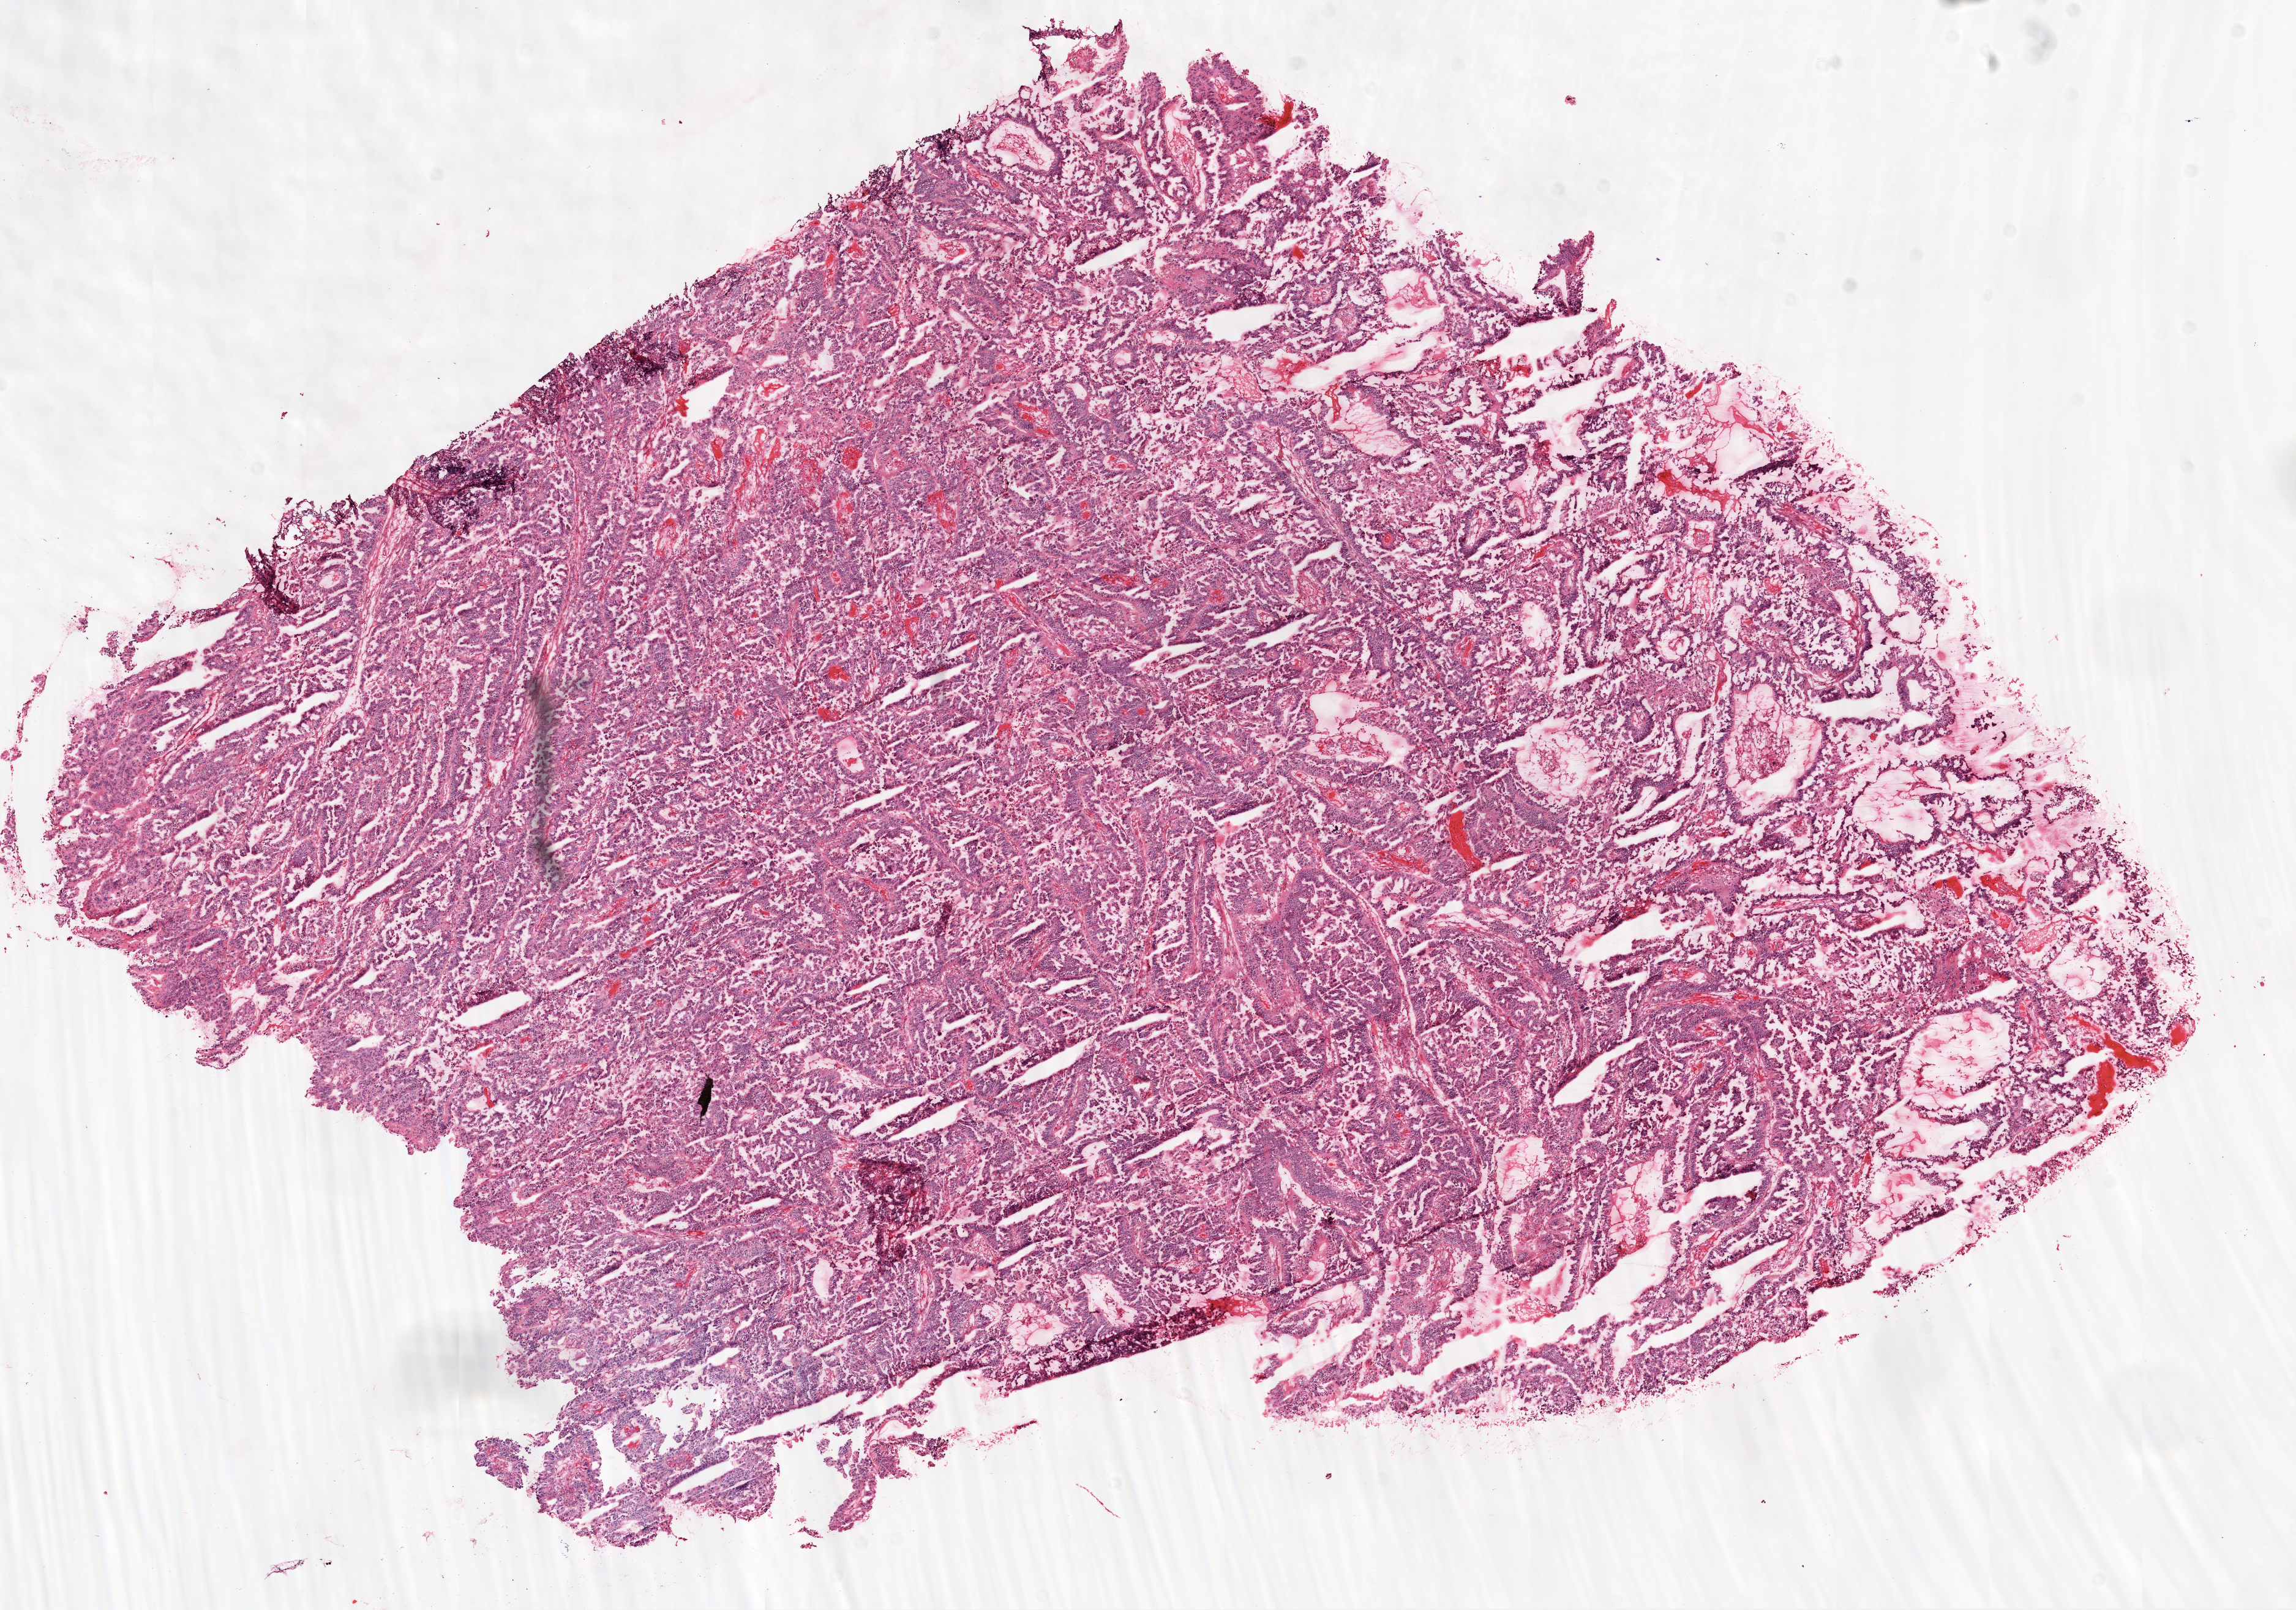
H&E-stained whole-slide image — a low-resolution overview of the entire scanned area, about 15.0 x 10.5 mm. Frozen section. Sample: primary tumour, ovary. Female, age 53 years at initial diagnosis. Histologic grade: G2 (moderately differentiated). Composition of this section per pathologist review: tumour cells 95%, tumour nuclei 90%, normal cells 0%, stromal cells 0%, necrosis 5%.
- laterality: bilateral
- histologic diagnosis: Serous cystadenocarcinoma, NOS
- FIGO stage: IIC